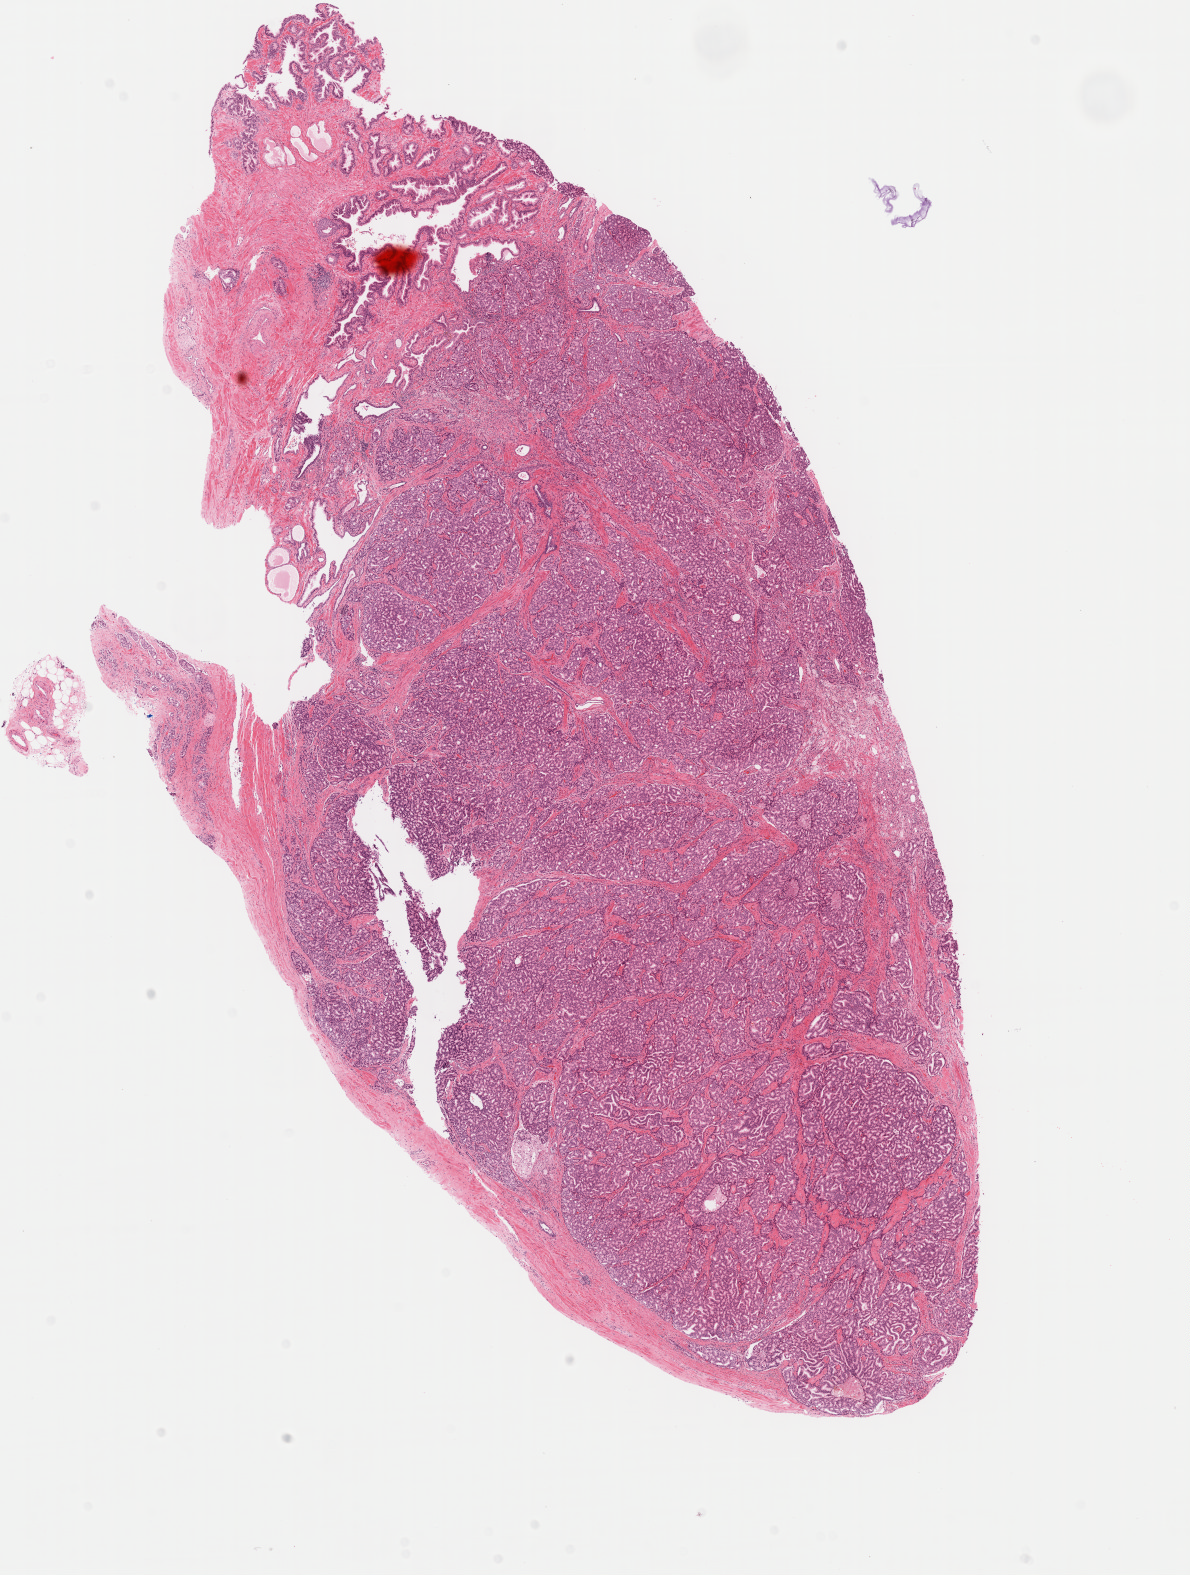
Hematoxylin and eosin (H&E) stained whole-slide image, low-resolution overview of the scanned area, about 9.4 x 12.4 mm (slide scanned at 40x). FFPE section. Prostate, primary tumour sample. Patient: male, age at initial diagnosis 77 years. Gleason score: 7 (4+3).
Laterality: bilateral. Pathologic diagnosis: Adenocarcinoma, NOS (prostate gland). Lymph nodes positive (case pathology): 0 of 10 examined.